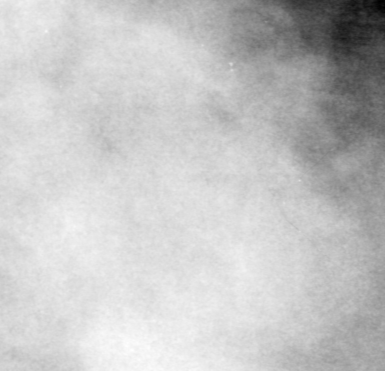
Region of interest cut from a scanned film mammogram (one marked finding); left breast; CC view; BI-RADS breast density category 3 (scale 1–4).
- Marked abnormality: mass, shape lobulated, margins obscured; BI-RADS assessment category 0; pathology (as recorded): benign.